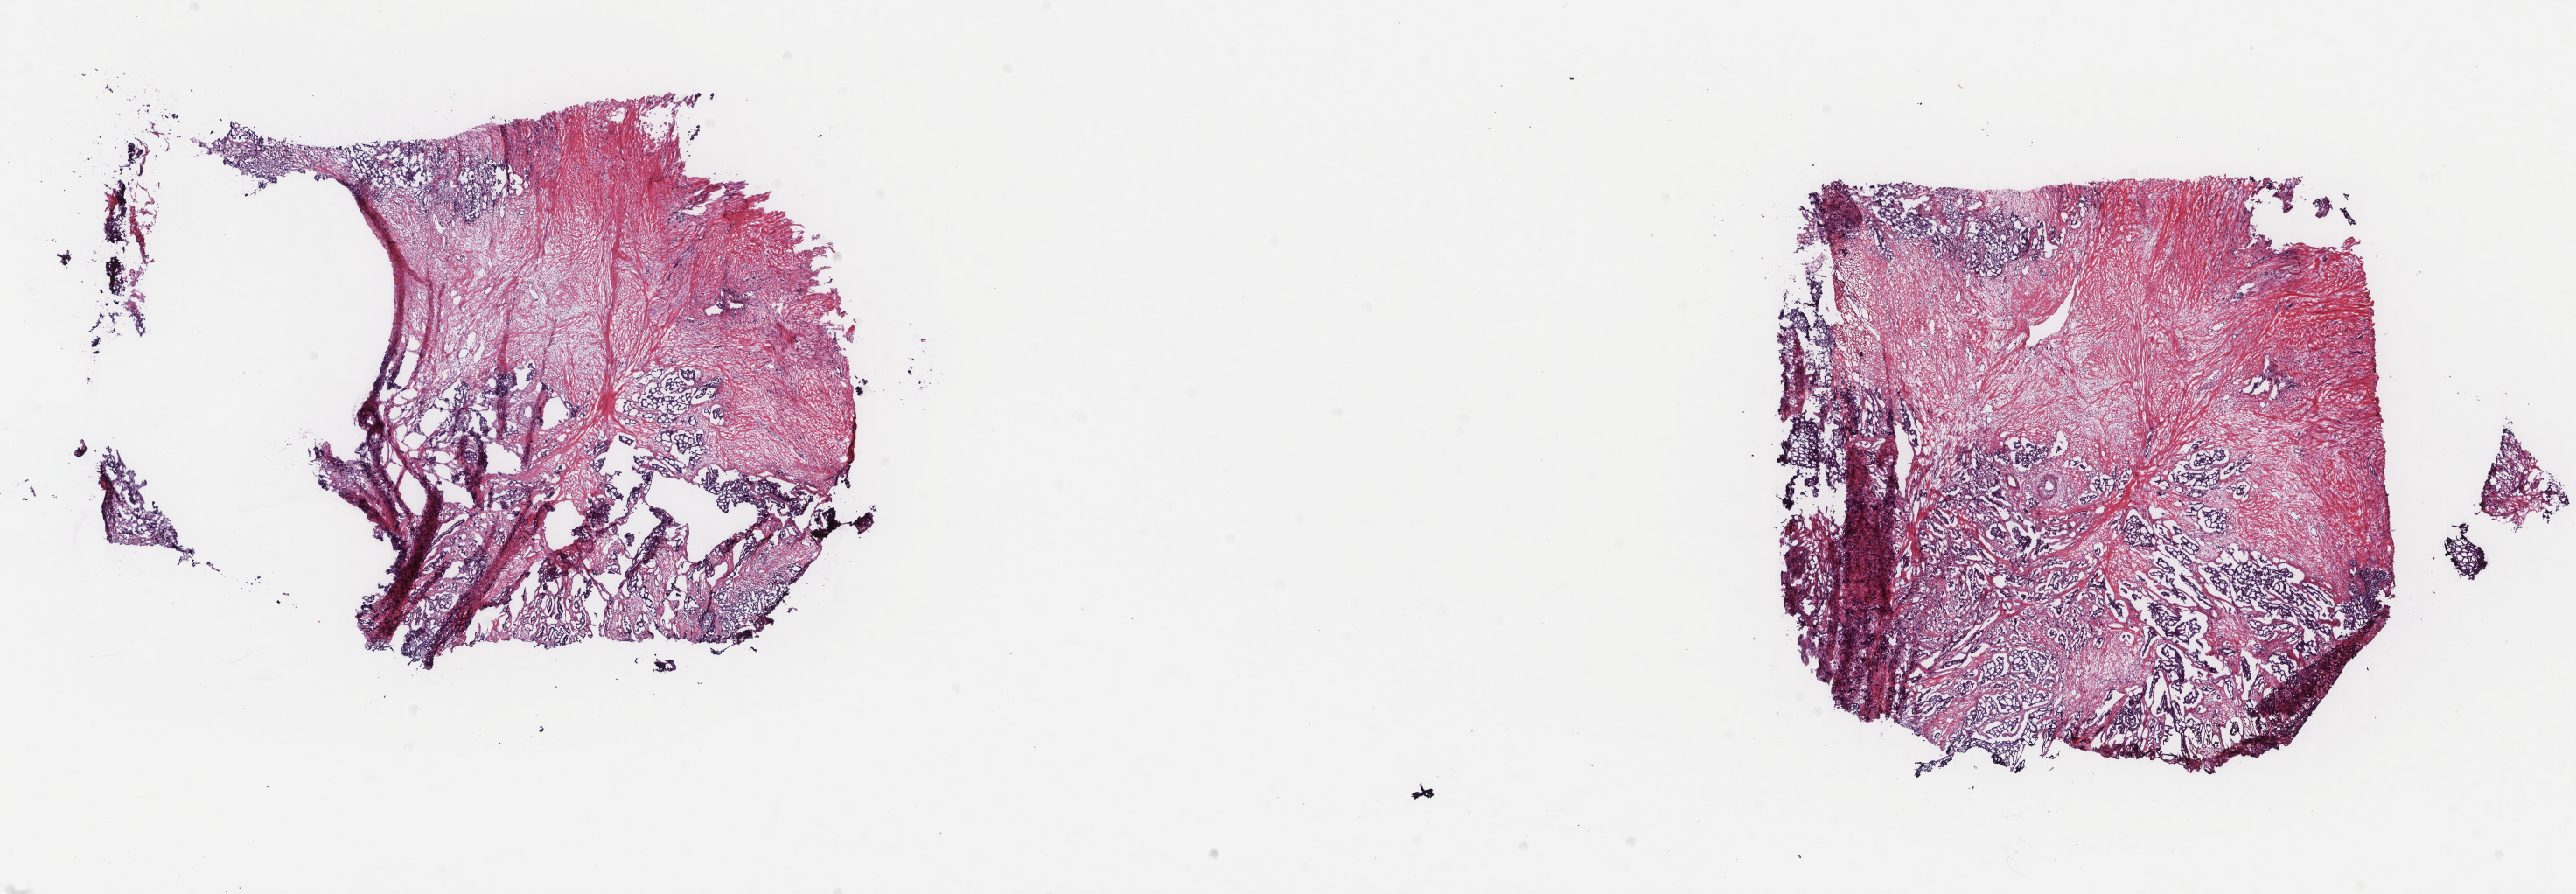
Whole-slide histology image, Hematoxylin and eosin (H&E) stained, a low-resolution overview of the entire scanned area, about 23.4 x 8.1 mm, frozen section from the top of the tissue portion, primary tumour sample from the breast. Female patient; age at initial diagnosis 39 years. Composition of this section per pathologist review: tumour cells 45%, tumour nuclei 80%, normal cells 0%, stromal cells 55%, necrosis 0%. Inflammatory infiltration, as recorded: lymphocyte infiltration 1%, monocyte infiltration 0%, neutrophil infiltration 0%.
AJCC pathologic stage: IIA. Histologic diagnosis: Infiltrating duct carcinoma, NOS. Laterality: right. Lymph nodes positive (case pathology): 0 of 5 examined.